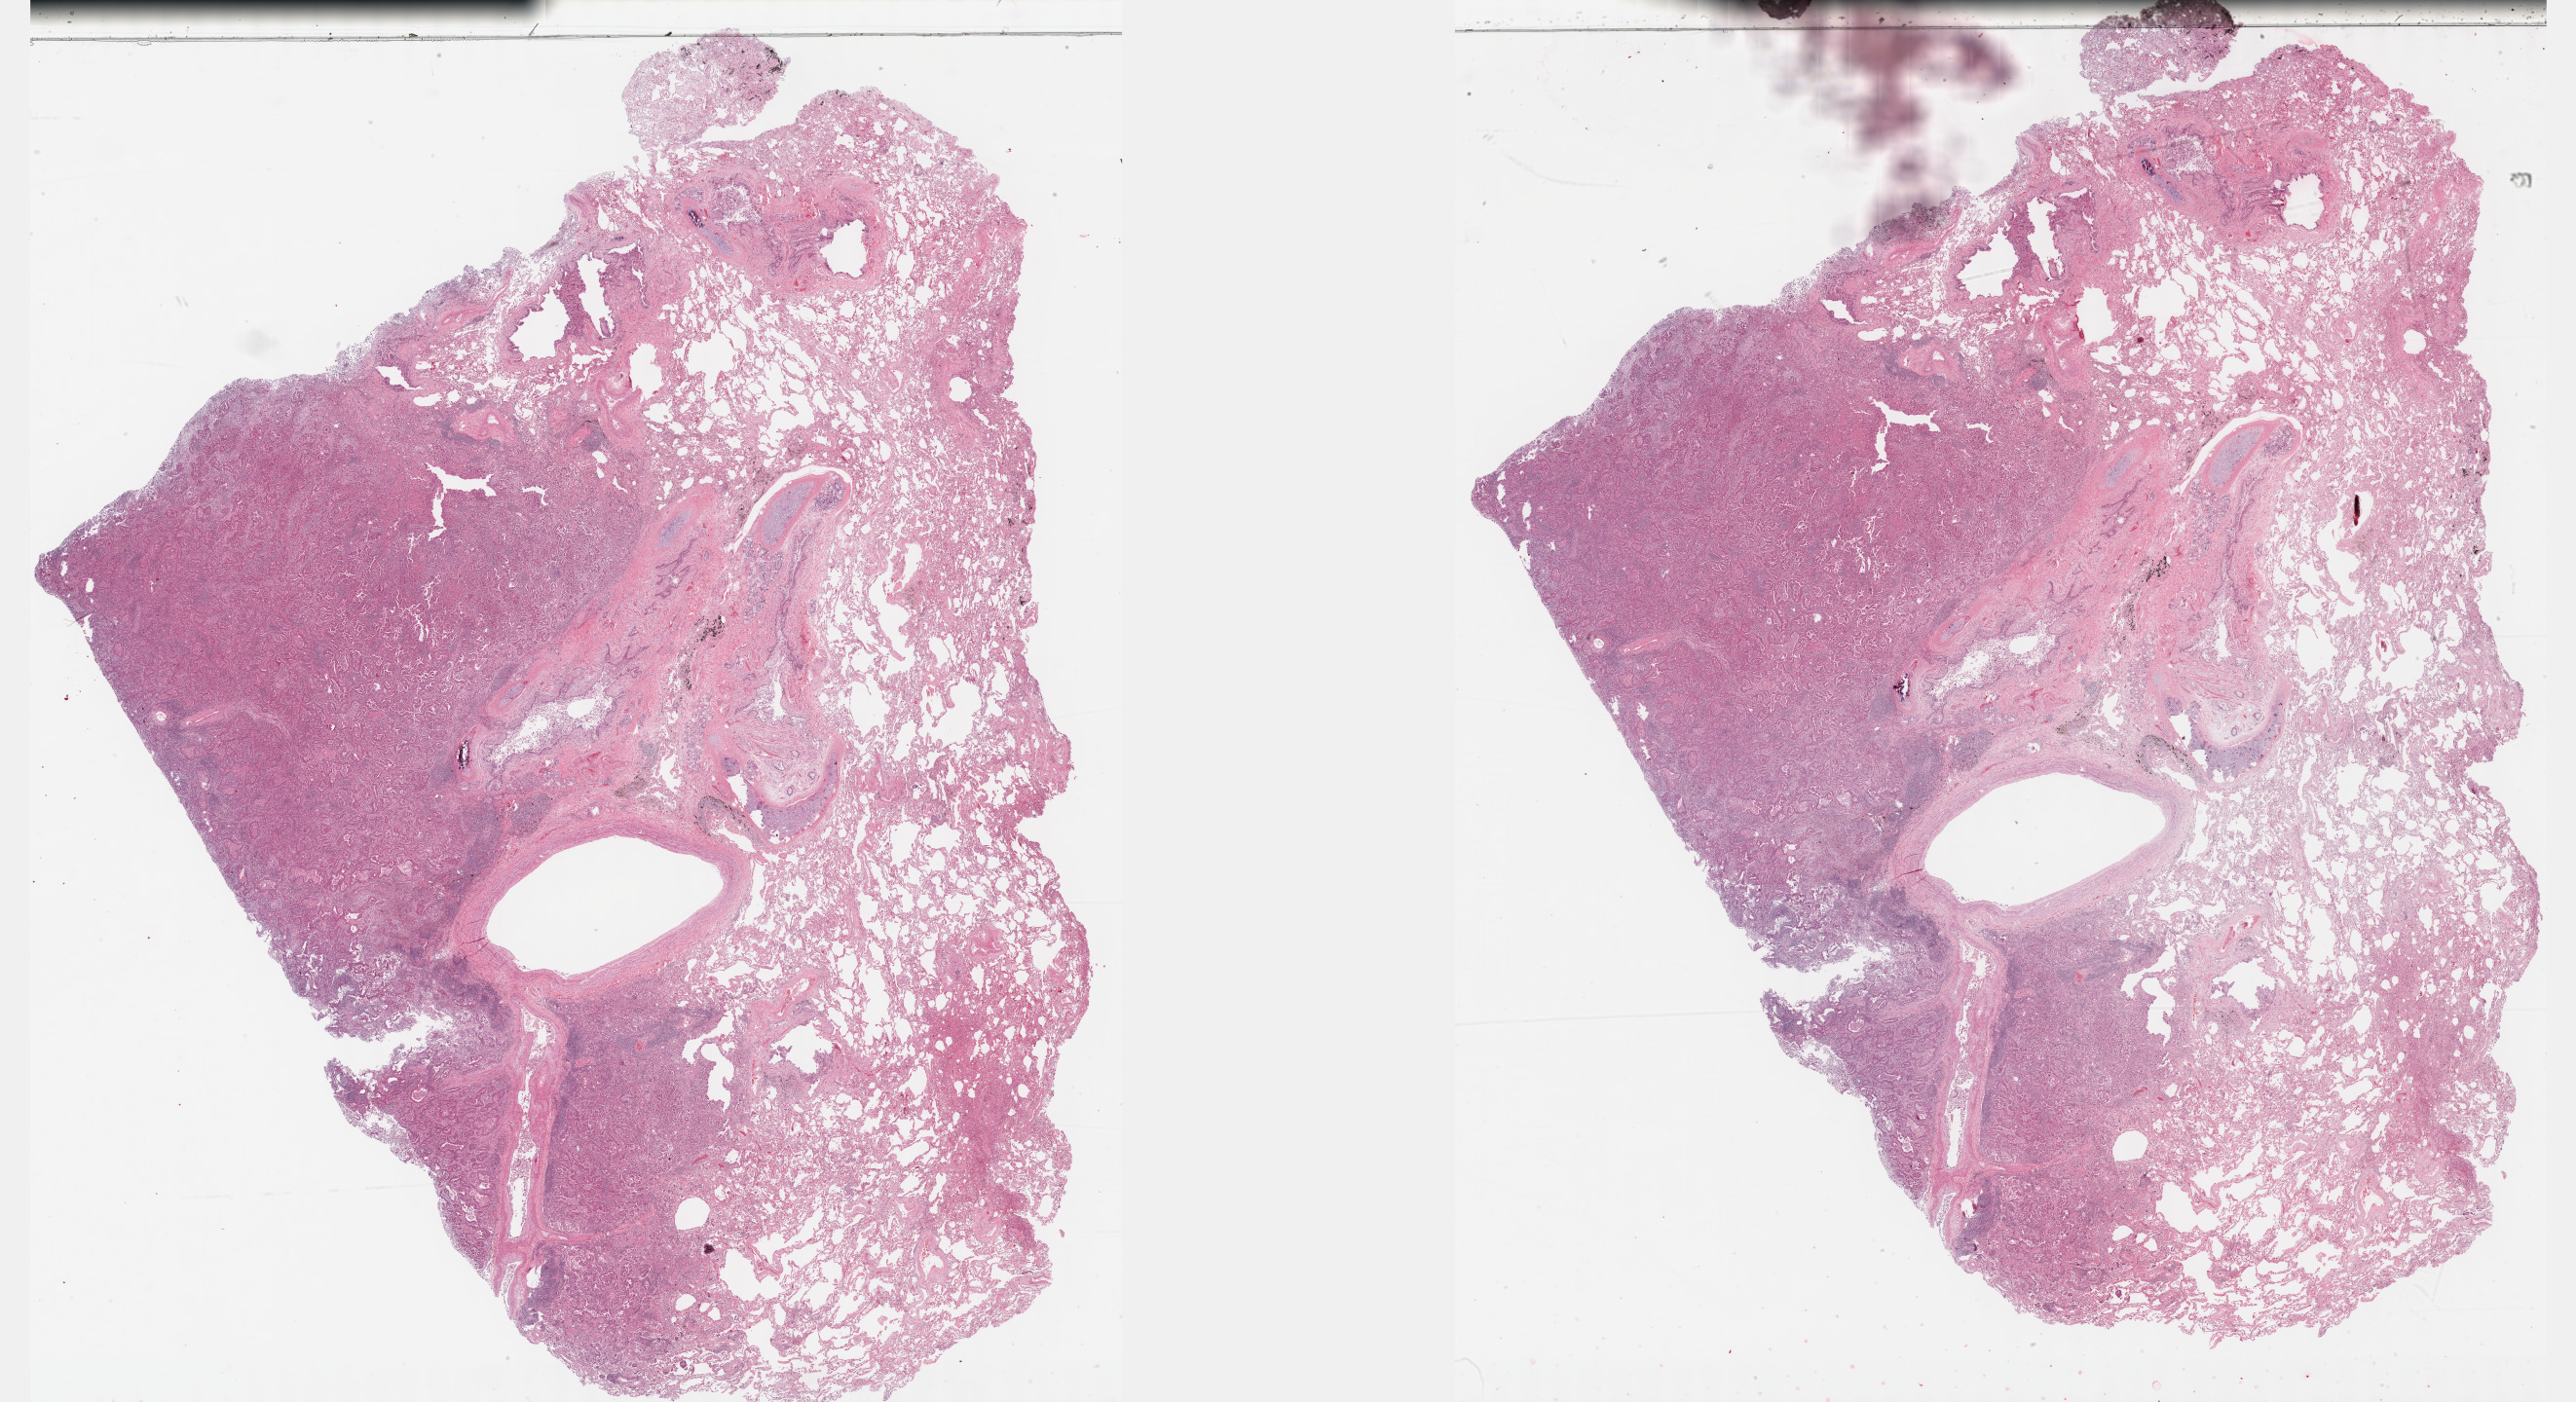
Hematoxylin and eosin (H&E) stained whole-slide image — a low-resolution overview of the entire scanned area, about 42.8 x 23.3 mm (slide scanned at 40x). Formalin-fixed paraffin-embedded (FFPE) diagnostic section. Primary tumour sample from the lung. Patient: female, age at initial diagnosis 59 years.
Laterality: right. Pathologic diagnosis: Adenocarcinoma, NOS (lower lobe, lung). AJCC pathologic stage: IIB.